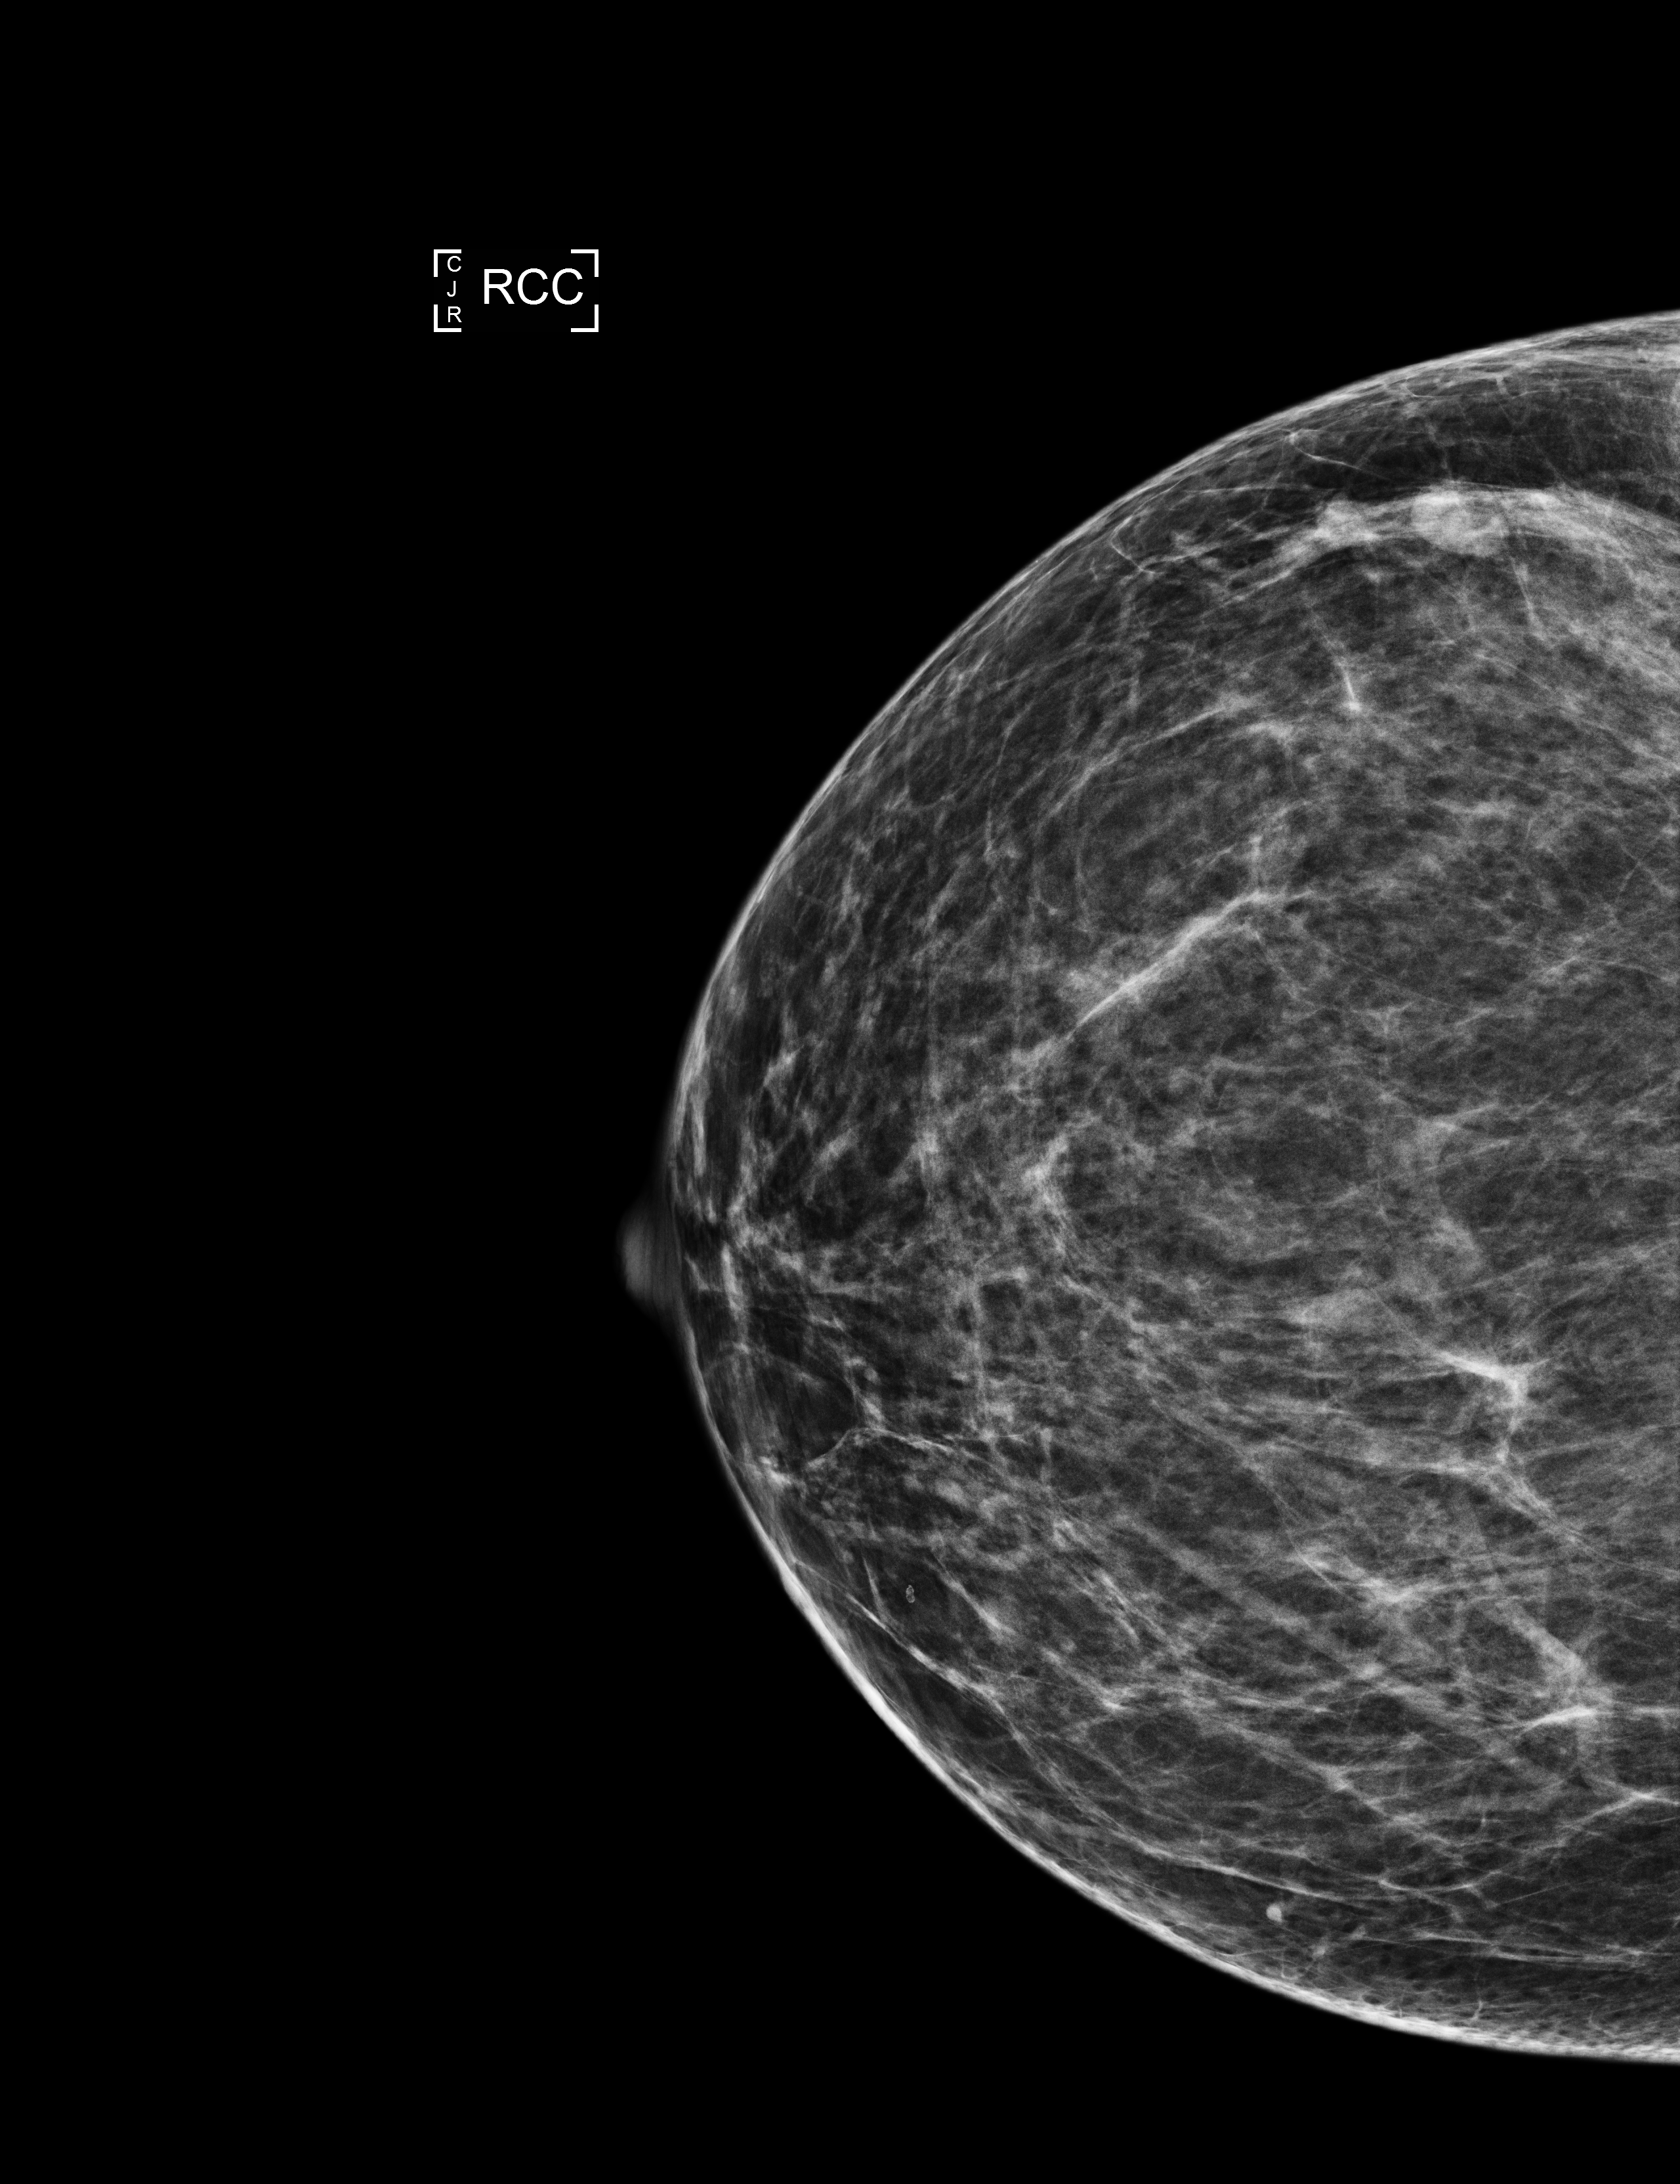
Digital mammogram (FFDM); right breast; cranio-caudal projection; annual screening mammography examination. Patient: female, 44 years.
Breast density at the screening exam (both breasts): heterogeneously dense (BI-RADS density category c). Final BI-RADS assessment for this screening round (tomosynthesis exam, both breasts): category 2. Recall: no recall after this screen.